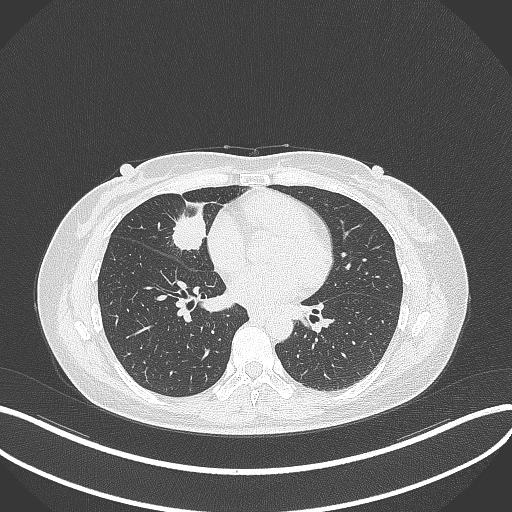
Chest CT, one axial slice; position 128 of 284 along the scan axis; lung window (W 1500 / L -600 HU); 1 mm slice thickness; 512 × 512 image matrix, field of view 400 × 400 mm. Female patient, age 43 years. Case-level facts recorded for this patient, not image findings: clinical TNM (as recorded): T1c N3 M1; histopathological grade: G1.
Structures marked on this image (rectangle marked by the reading radiologist):
- lung tumour (recorded histology: adenocarcinoma): box from (x=168, y=208) to (x=208, y=256) px